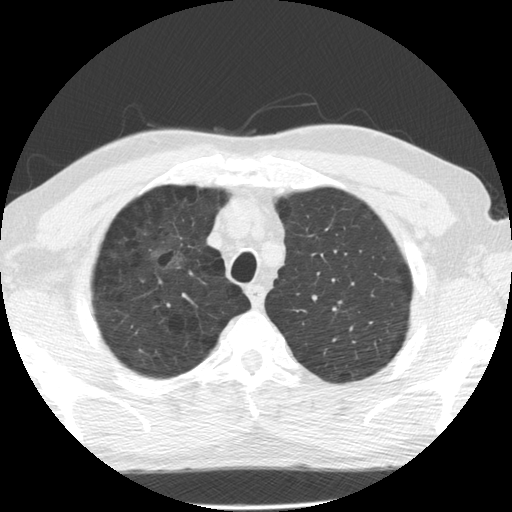
Low-dose screening chest CT, axial slice. Second annual screen. Lung window (W 1500 / L -600 HU). Slice 106 of 135 in the series. 512 × 512 image matrix. Male participant, aged 60 years at enrolment. Former smoker at enrolment.
• Expert reader's lesion annotation, bounding box (x1, y1, x2, y2) in pixels: (134, 235, 189, 293).
• Reader record for this screening exam (exam-level; its link to the box is not recorded): non-calcified nodule or mass ≥4 mm, right upper lobe, poorly defined margins, mixed attenuation, pre-existing on the prior screen: yes; interval growth: yes.
• Official screen result: positive, other.